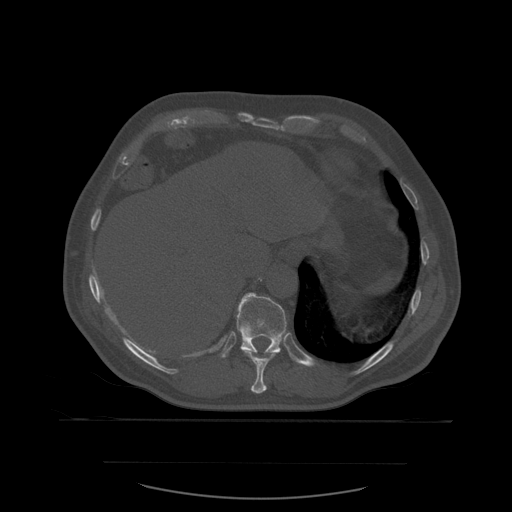
CT including the spine, one axial slice; slice 307 of 590 in the series (ordered by position); bone window (W 1800 / L 400 HU); 1.25 mm slice thickness; 512 × 512 image matrix. Patient age 71 years. Case-level facts recorded for this patient, not image findings: primary cancer: lung; vertebrae with lytic lesions (as recorded): T1, T2, L5, S1.
Outlined on this slice (semi-automatically segmented with operator editing):
- T10 vertebra: bounding box [x1, y1, x2, y2] px = [246, 352, 277, 394]
- T11 vertebra: [234, 293, 290, 367]